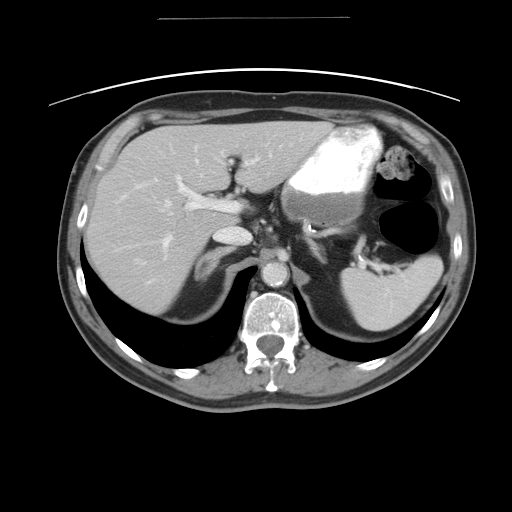
Contrast-enhanced abdominal CT, one axial slice; position 31 of 49 along the scan axis; reconstruction kernel STANDARD; intravenous contrast given; soft-tissue window (W 400 / L 40 HU); 5 mm slice thickness; 512 × 512 image matrix, field of view 413 × 413 mm. Male patient, age 57 years. From the clinical record (not read from this slice): diagnosis: colorectal cancer liver metastases, imaged before liver resection.
Outlined on this slice (outlined manually by an expert reader):
- hepatic veins: bounding box (x1, y1, x2, y2) in pixels: (134, 153, 270, 263)
- liver: (85, 121, 332, 313)
- planned liver remnant (the part of the liver to remain after resection): (209, 121, 332, 228)
- portal vein (with intrahepatic branches): (120, 156, 258, 248)